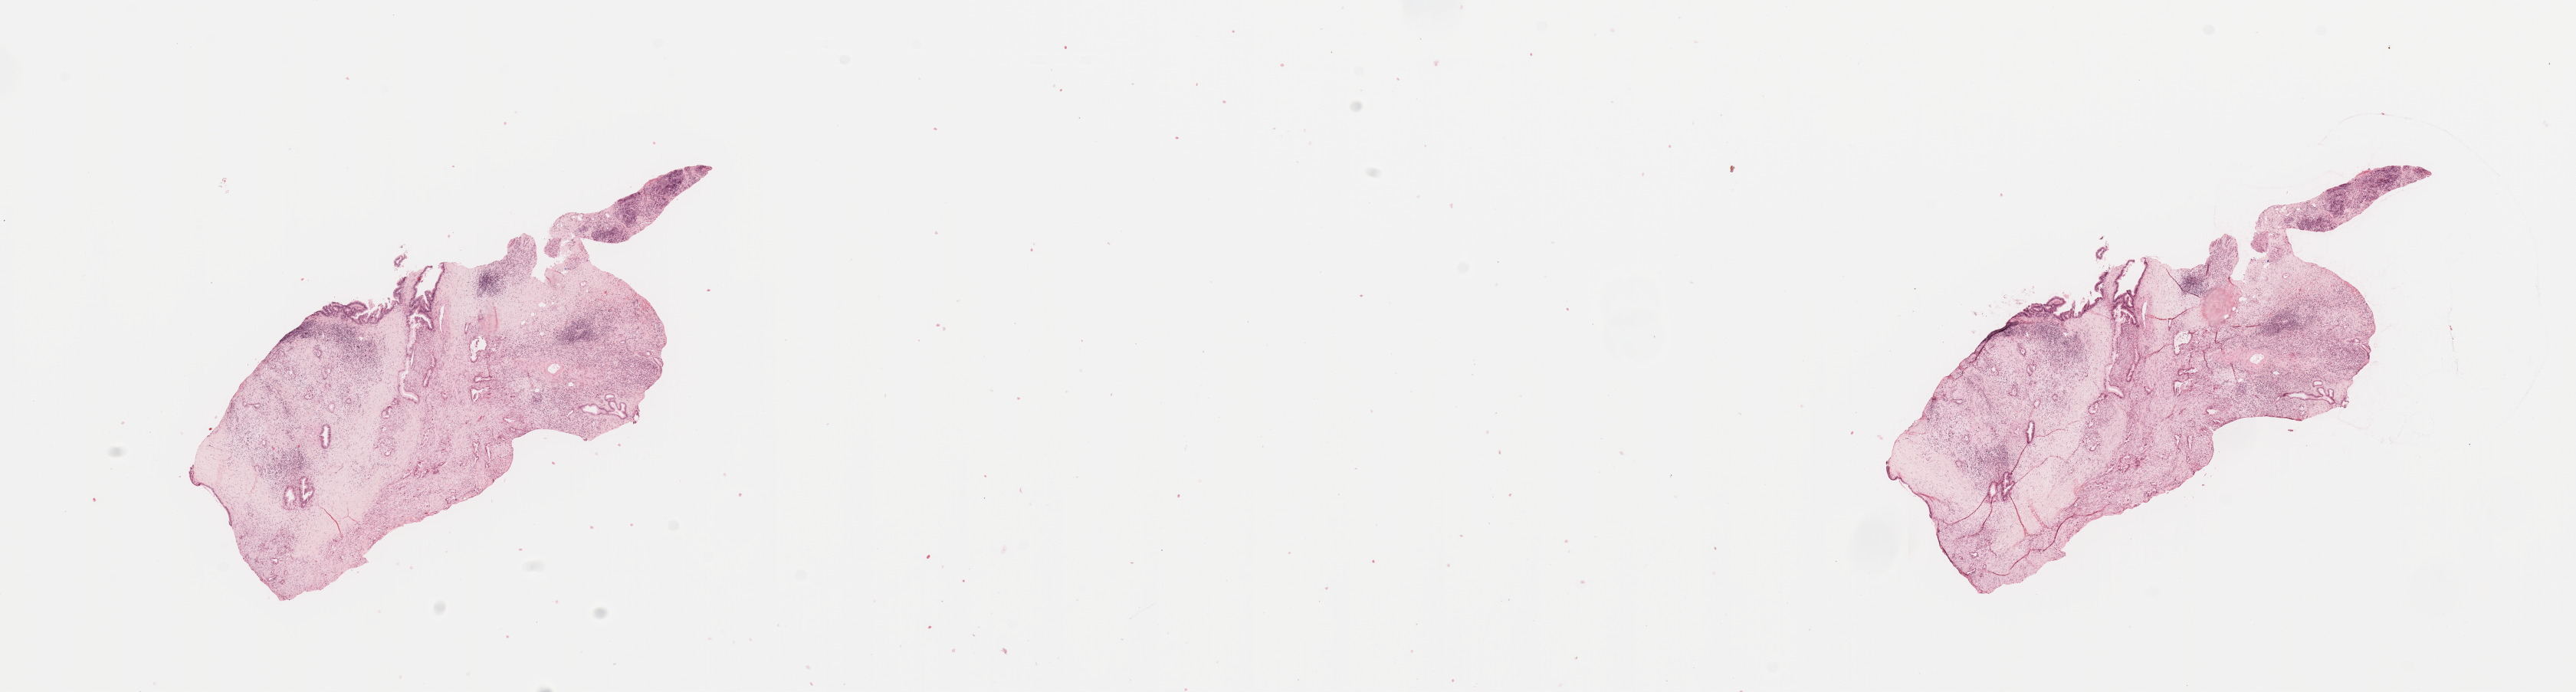
Whole-slide histology image, H&E-stained — shown as a low-resolution overview of the whole scanned area (about 26.6 x 7.1 mm). Tumour tissue sample, sampled site: pancreas. 71-year-old male patient. Histologic grade: G2 (moderately differentiated). Composition of this section per pathologist review: tumour nuclei 60%, necrosis 0%.
- histologic diagnosis: Infiltrating duct carcinoma, NOS
- AJCC pathologic stage: IB
- primary tumour site (as recorded): head